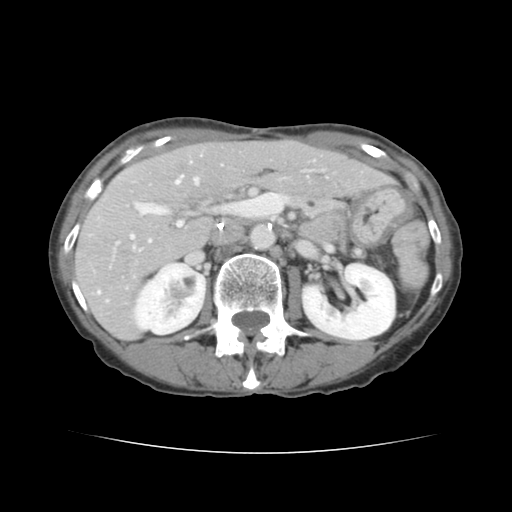
Contrast-enhanced abdominal CT, one axial slice. Position 72 of 136 along the scan axis. Soft-tissue window (W 400 / L 40 HU). 512 × 512 image matrix, field of view 319 × 319 mm. Female patient, age 77 years. From the clinical record (not read from this slice): diagnosis: colorectal cancer liver metastases, imaged before liver resection; multiple liver metastases: yes.
Outlined on this slice (outlined manually by an expert reader):
- hepatic veins: box from (x=130, y=176) to (x=198, y=238) px
- liver: (x=76, y=142)–(x=387, y=338)
- planned liver remnant (the part of the liver to remain after resection): (x=157, y=142)–(x=388, y=200)
- portal vein (with intrahepatic branches): (x=98, y=205)–(x=182, y=293)